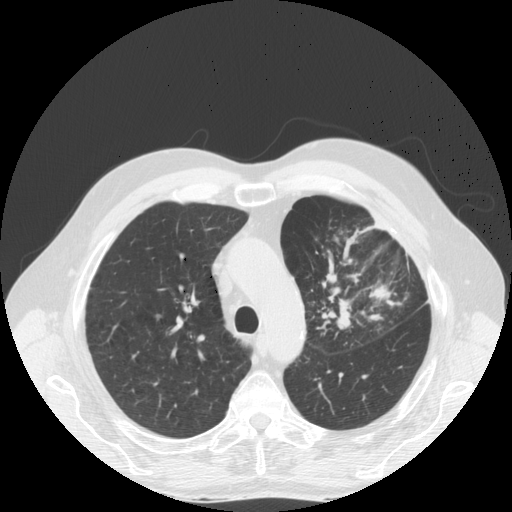
Low-dose screening chest CT, one axial slice. Position 127 of 170 along the scan axis. 140 kVp. Lung window (W 1500 / L -600 HU). 512 × 512 image matrix, field of view 380 × 380 mm.
Structures marked on this image (expert manual segmentation):
- lesion 1 (tumor, upper lobe of left lung): bounding box (x1, y1, x2, y2) in pixels: (337, 299, 352, 330)